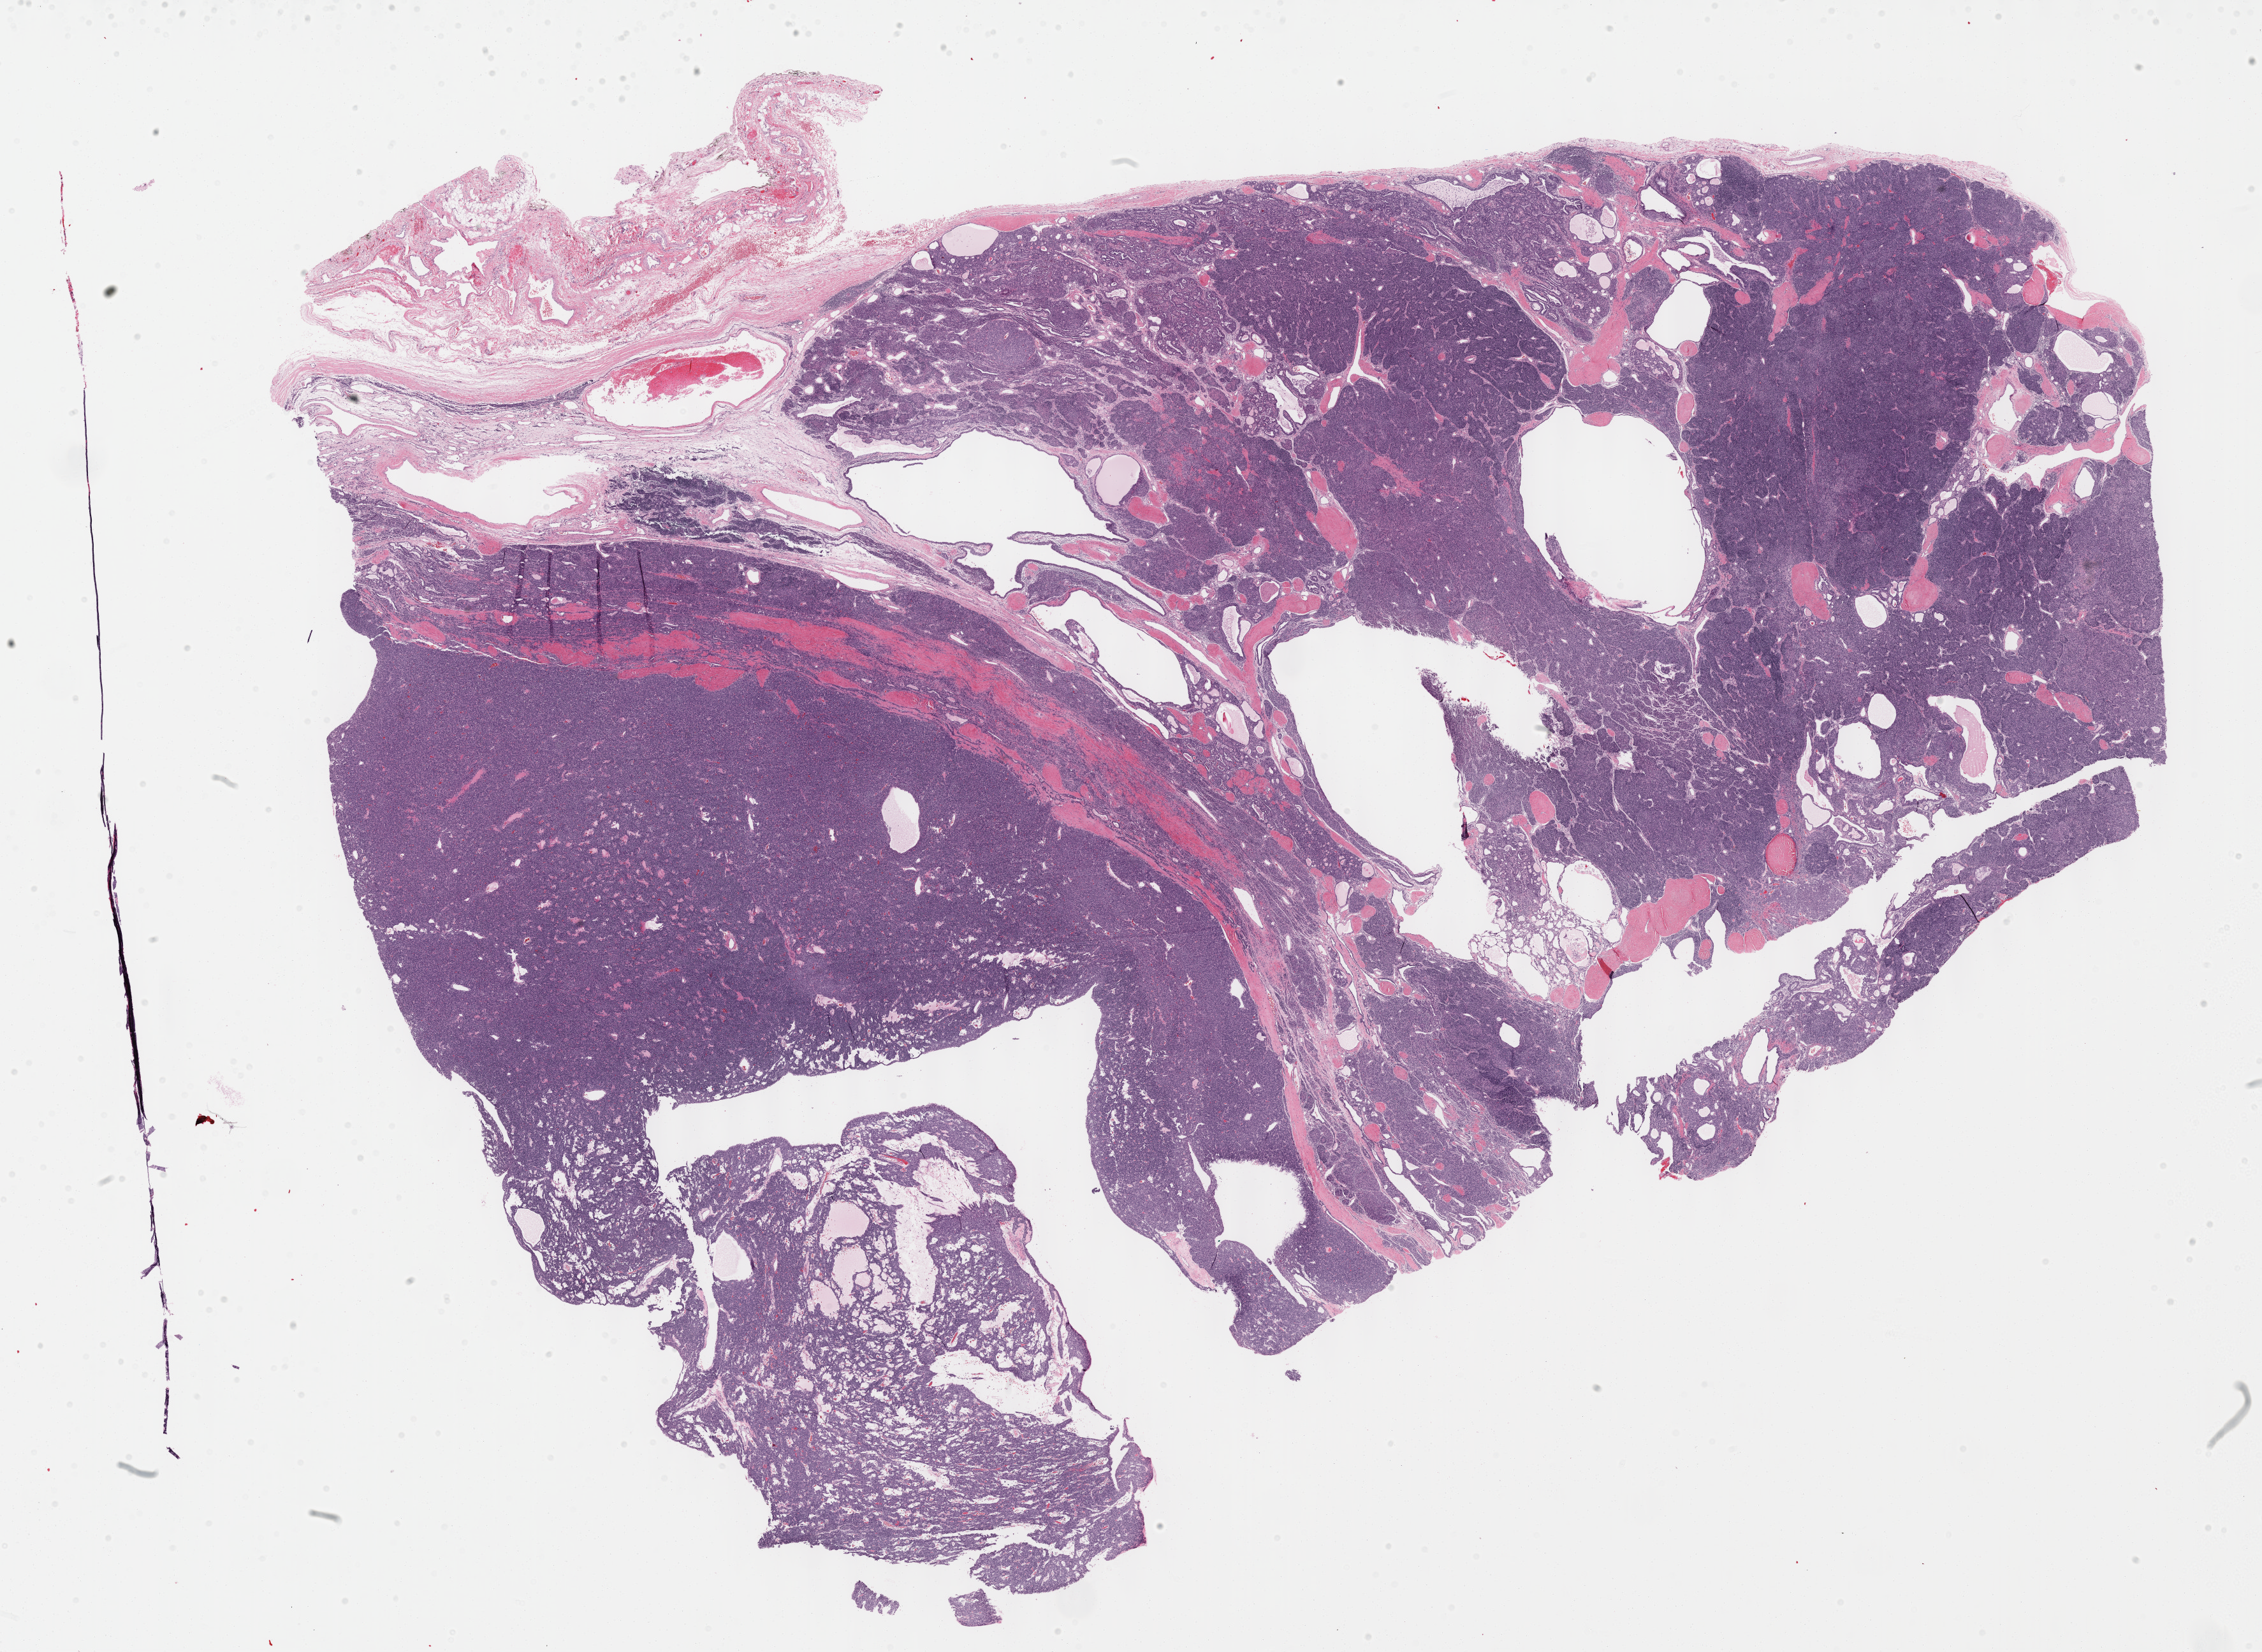
Digitized H&E-stained tissue section (whole slide), low-resolution overview of the scanned area, about 28.7 x 20.9 mm (acquisition: 40x scan), formalin-fixed paraffin-embedded (FFPE) diagnostic section, thymus, primary tumour sample. Male patient; age at initial diagnosis 64 years.
Histologic diagnosis: Thymoma, type AB, malignant (anterior mediastinum).